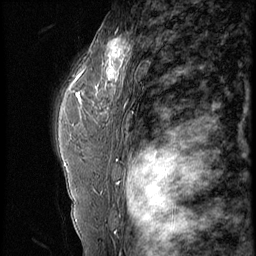
Breast MRI (dynamic contrast-enhanced), one sagittal slice; slice 42 of 56 in the series (ordered by position); 4 images stored at this slice position (order not interpretable as contrast timing); 1.5 T; TE 4.2 ms, TR 9 ms; 2.5 mm slice thickness; 256 × 256 image matrix, field of view 180 × 180 mm. Patient: female, 44 years. Case-level facts recorded for this patient, not image findings: setting: breast cancer imaged before/during neoadjuvant chemotherapy; receptor status: triple-negative.
Structures marked on this image (semi-automatic segmentation, software-assisted and operator-edited):
- analysis volume of interest (the breast-tissue region the enhancement analysis was run in; not a lesion): bounding box <87,28,132,99> (left, top, right, bottom; pixels)
- tumour enhancement mask (voxels above the 140 % enhancement threshold inside the analysis volume of interest): <97,39,129,90>